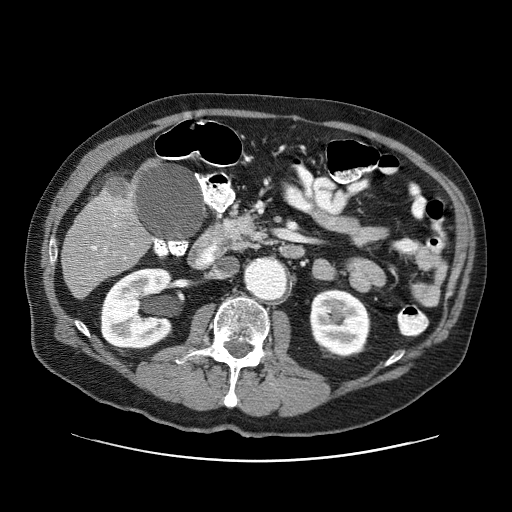
Contrast-enhanced abdominal CT (liver protocol), one axial slice; slice 18 of 87 in the series (ordered by position); 120 kVp; one of 3 acquisitions stored at this slice position; soft-tissue window (W 400 / L 40 HU); 2.5 mm slice thickness; 512 × 512 image matrix, field of view 400 × 400 mm. Case-level facts recorded for this patient, not image findings: diagnosis: hepatocellular carcinoma (patient treated with transarterial chemoembolisation; whether this scan precedes or follows treatment is not stated here); TNM stage (as recorded): Stage-IIIA; Child-Pugh class: A; tumour differentiation: well differentiated; tumour nodularity: multinodular.
Annotated regions visible in this slice (semi-automatic segmentation, software-assisted and operator-edited):
- liver parenchyma outside the tumour (the mass and vessels are separate outlines, so this box may not span the whole liver): bounding box (x1, y1, x2, y2) in pixels: (62, 176, 148, 298)
- mass: (103, 175, 135, 214)
- liver vessels: (92, 208, 133, 264)